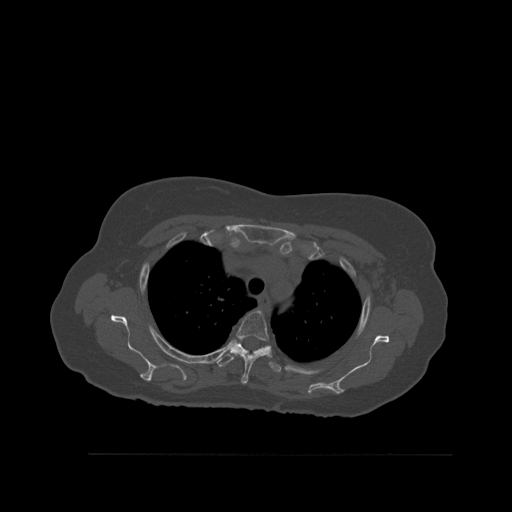
CT including the spine, one axial slice; position 416 of 527 along the scan axis; bone window (W 1800 / L 400 HU); 1.5 mm slice thickness; 512 × 512 image matrix, field of view 470 × 470 mm. Female patient, age 73 years. Case-level facts recorded for this patient, not image findings: primary cancer: breast; vertebrae with lytic lesions (as recorded): L2.
Annotated regions visible in this slice (semi-automatically segmented with operator editing):
- T3 vertebra: box from (x=235, y=311) to (x=271, y=384) px
- T4 vertebra: (x=217, y=339)–(x=282, y=373)